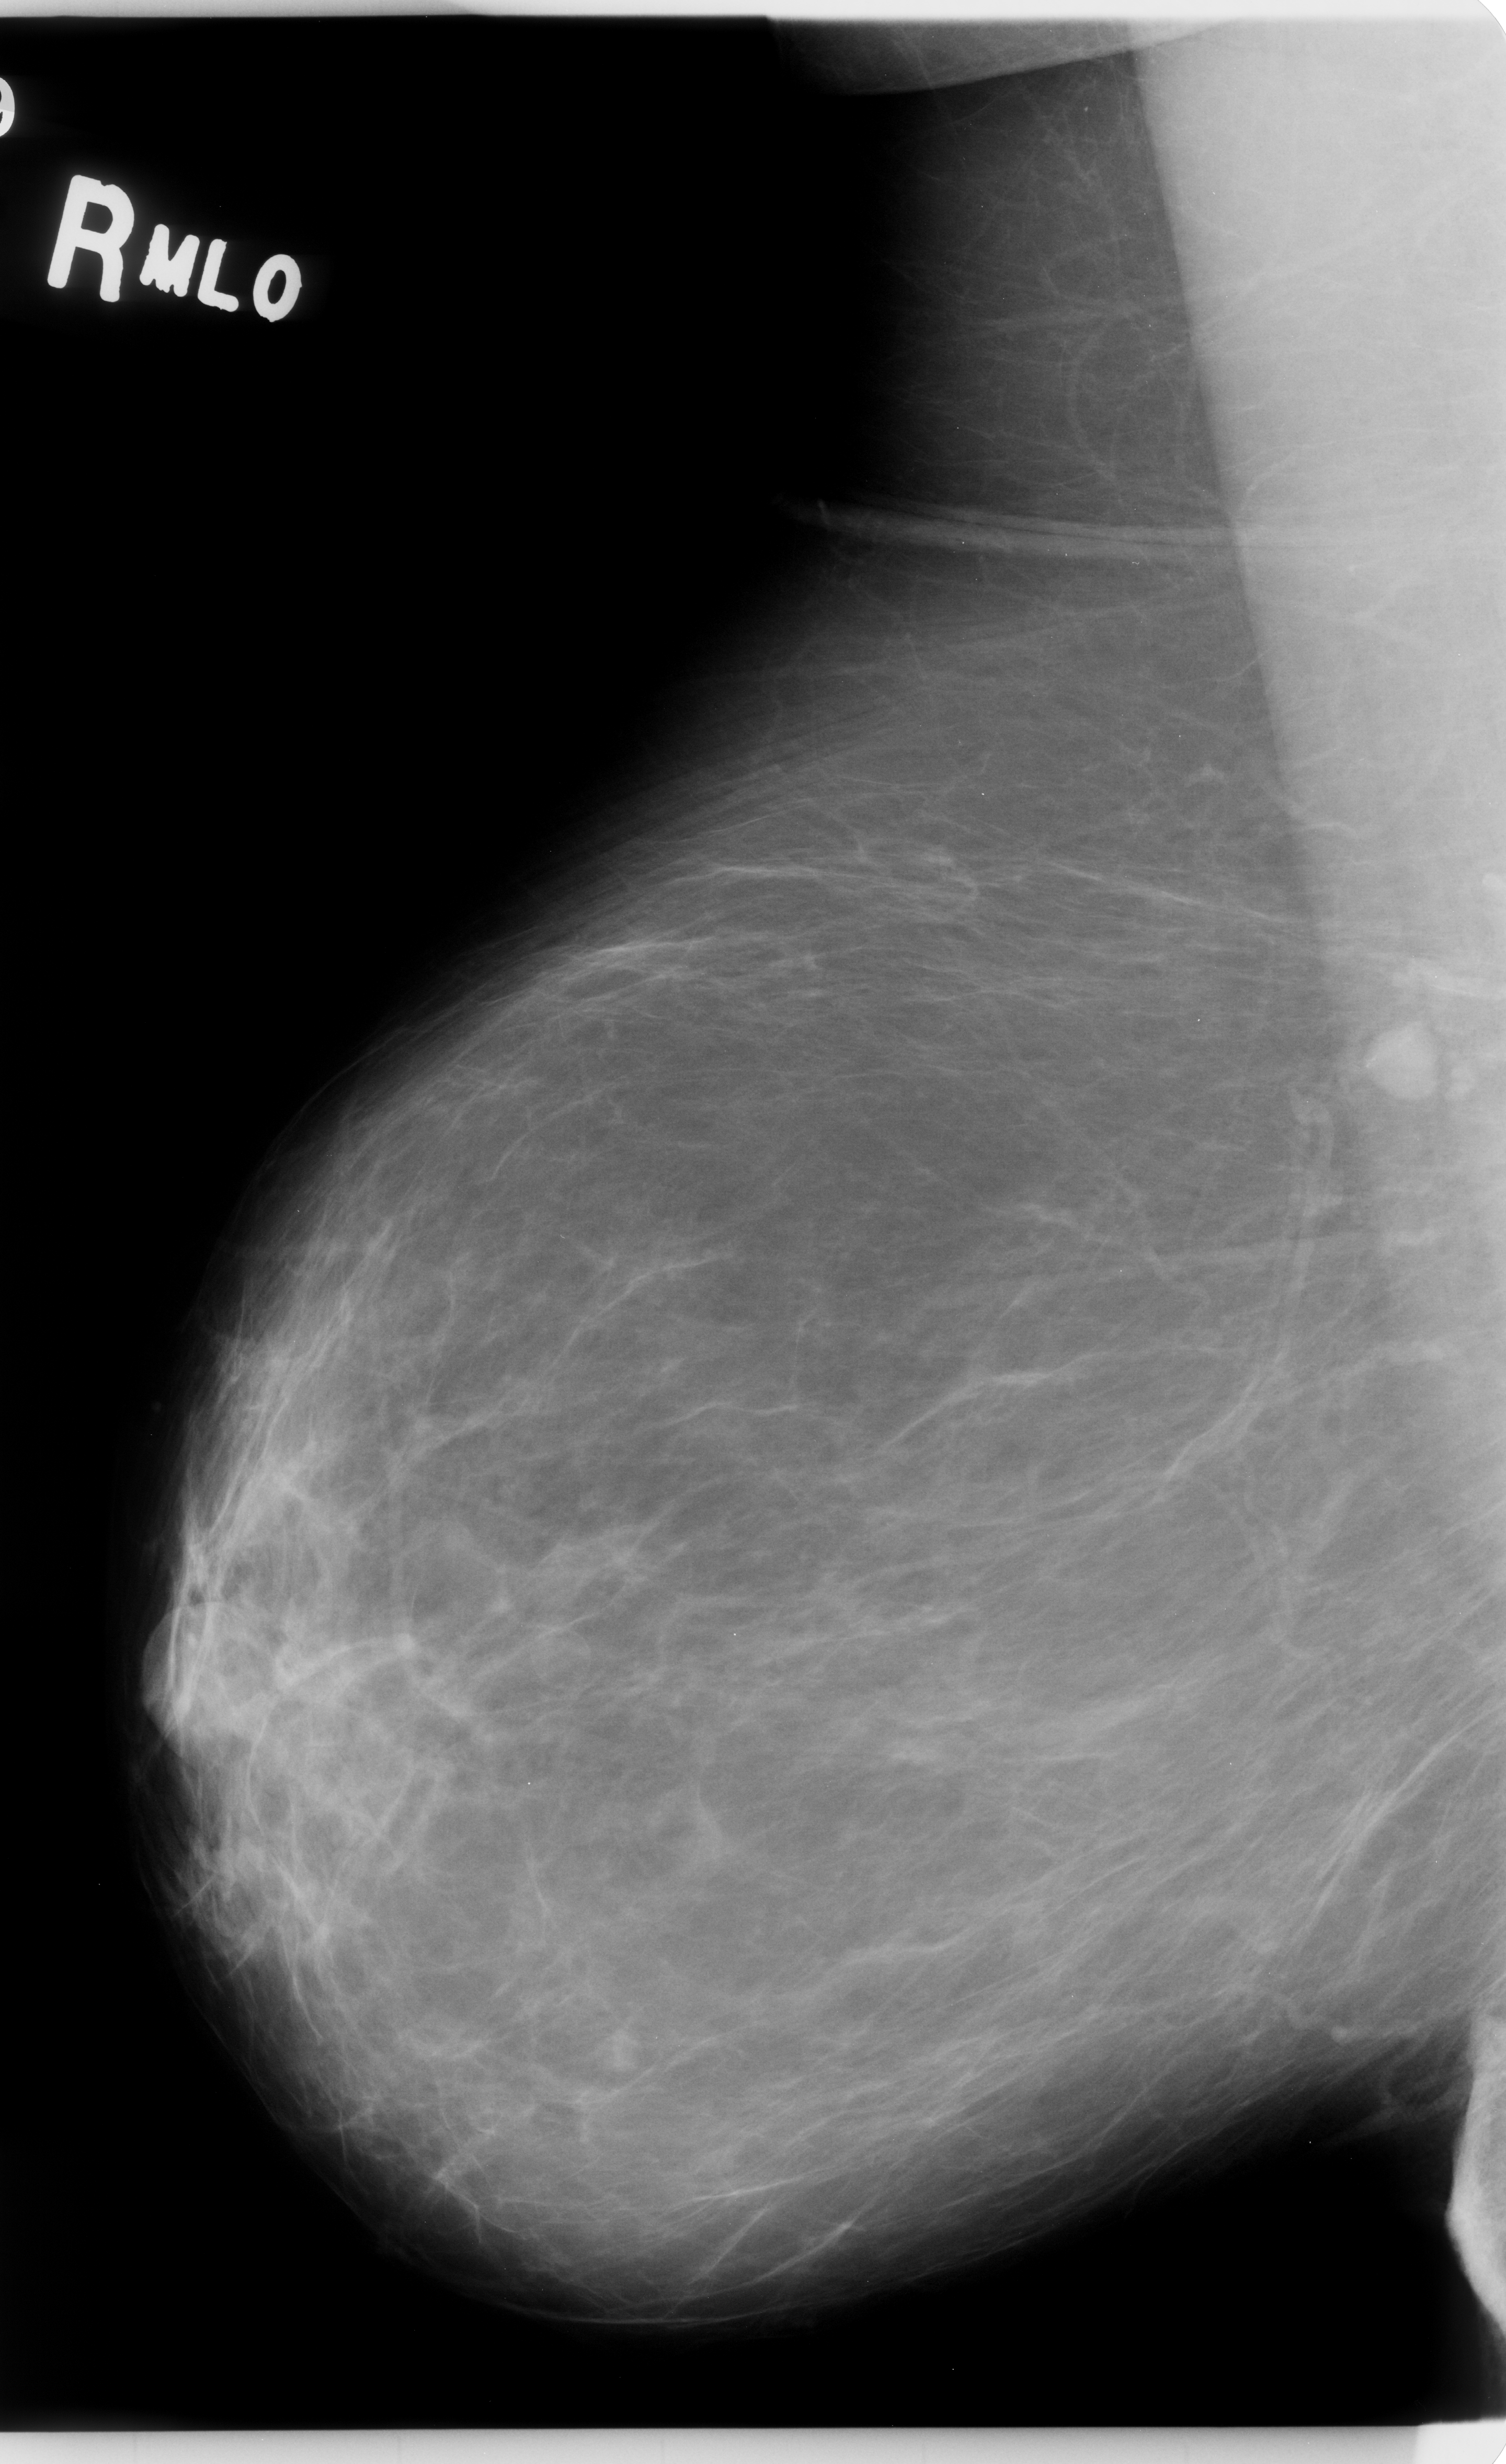
Digitized screen-film mammogram; right breast; mediolateral oblique (MLO) view.
Mass, shape oval, margins circumscribed; BI-RADS assessment category 3; pathology (as recorded): benign.